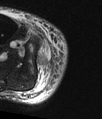
MRI of an extremity soft-tissue mass, one axial slice; slice 10 of 48 in the series (ordered by position); T2-weighted fat-saturated; MR volume resampled by the dataset authors to the PET/CT grid (not the native acquisition matrix); 3.27 mm slice thickness; 102 × 119 image matrix, field of view 100 × 116 mm. Male patient. From the clinical record (not read from this slice): histological type: pleiomorphic liposarcoma; grade: high; site of the primary tumour: right calf.
Annotated regions visible in this slice (expert contour drawn on MRI and transferred to this co-registered scan by the dataset authors):
- gross tumour volume including surrounding oedema: box from (x=39, y=58) to (x=47, y=66) px